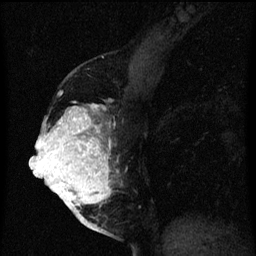
Breast MRI (dynamic contrast-enhanced), one sagittal slice; slice 28 of 60 in the series (ordered by position); dynamic contrast-enhanced series, image 2 of 3 at this slice position (ordered by acquisition); 1.5 T; TE 4.2 ms, TR 8 ms; 2 mm slice thickness; 256 × 256 image matrix. Patient: female, 56 years.
Outlined on this slice (semi-automatically segmented with operator editing):
- analysis volume of interest (the breast-tissue region the enhancement analysis was run in; not a lesion): box from (x=40, y=106) to (x=123, y=219) px
- tumour enhancement mask (voxels above the 70 % enhancement threshold inside the analysis volume of interest): (x=40, y=106)–(x=115, y=219)